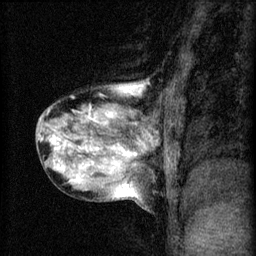
Breast MRI (dynamic contrast-enhanced), one sagittal slice; position 26 of 60 along the scan axis; 3 images stored at this slice position (order not interpretable as contrast timing); 1.5 T; TE 4.2 ms, TR 8.2 ms; 2 mm slice thickness; 256 × 256 image matrix. Female patient, age 40 years.
Structures marked on this image (semi-automatic segmentation, software-assisted and operator-edited):
- analysis volume of interest (the breast-tissue region the enhancement analysis was run in; not a lesion): bounding box (x1, y1, x2, y2) in pixels: (35, 80, 167, 211)
- tumour enhancement mask (voxels above the 70 % enhancement threshold inside the analysis volume of interest): (50, 88, 146, 183)